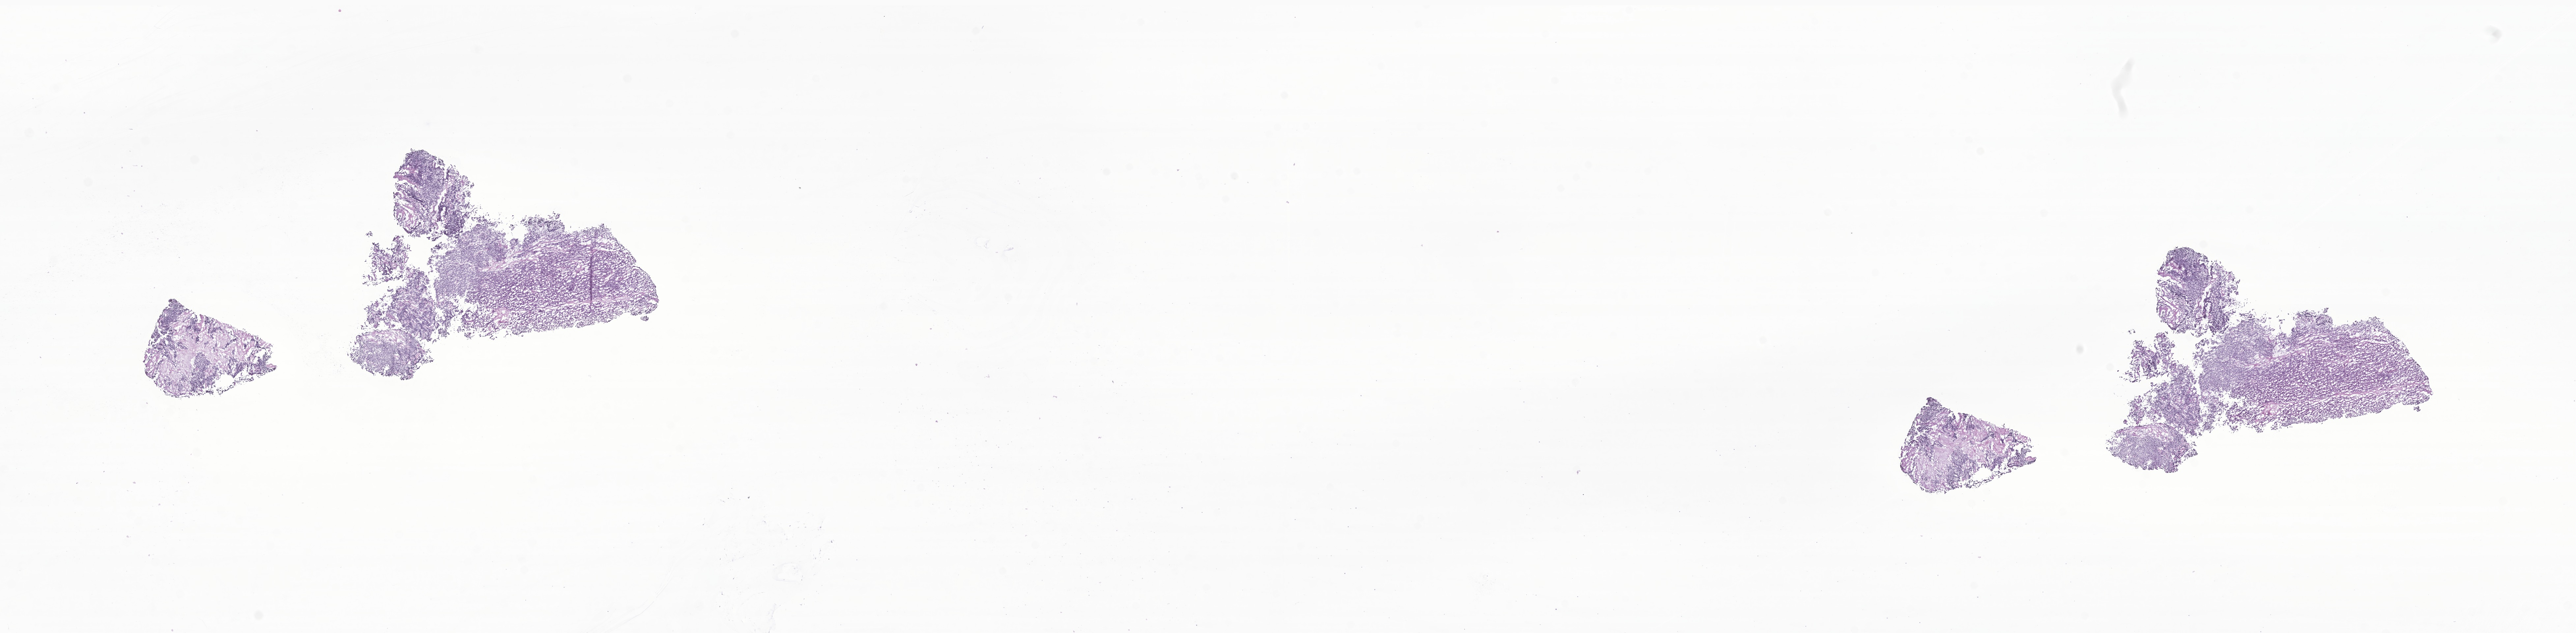
Whole-slide image, haematoxylin and eosin stain of tumor tissue from the brain — shown as a low-resolution overview of the whole scanned area (about 33.0 x 8.1 mm); cryosection (OCT / tissue freezing medium). Male patient, age 182 months (15 years 2 months).
Recorded diagnosis: Medulloblastoma, NOS.